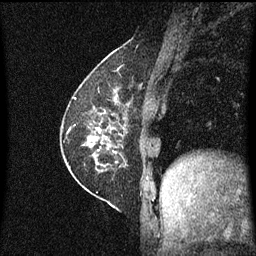
Breast MRI (dynamic contrast-enhanced), one sagittal slice. Slice 22 of 60 in the series (ordered by position). Dynamic contrast-enhanced series, image 2 of 3 at this slice position (ordered by acquisition). 1.5 T. TE 4.2 ms, TR 8.4 ms. 256 × 256 image matrix. Female patient, age 60 years.
Annotated regions visible in this slice (semi-automatically segmented with operator editing):
- analysis volume of interest (the breast-tissue region the enhancement analysis was run in; not a lesion): bounding box [x1, y1, x2, y2] px = [69, 66, 134, 193]
- tumour enhancement mask (voxels above the 70 % enhancement threshold inside the analysis volume of interest): [88, 96, 129, 165]